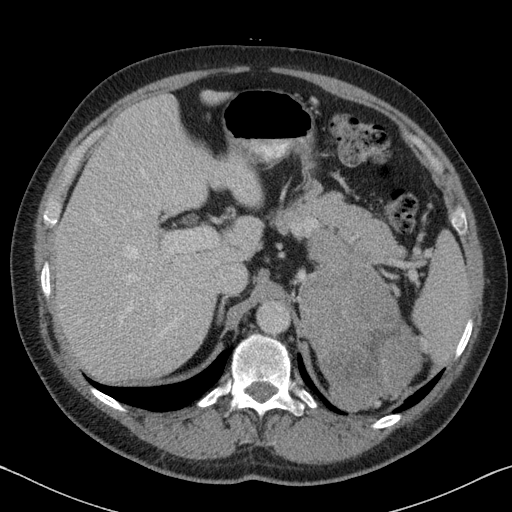
Contrast-enhanced abdominal CT, one axial slice. Position 57 of 88 along the scan axis. Reconstruction kernel B31f. 120 kVp. Intravenous contrast given. Soft-tissue window (W 400 / L 40 HU). 3 mm slice thickness. 512 × 512 image matrix, field of view 366 × 366 mm. Male patient, age 51 years. Case-level facts recorded for this patient, not image findings: diagnosis: adrenocortical carcinoma; tumour side: left adrenal.
Outlined on this slice (semi-automatic segmentation, software-assisted and operator-edited):
- mass: bounding box (x1, y1, x2, y2) in pixels: (299, 231, 418, 407)